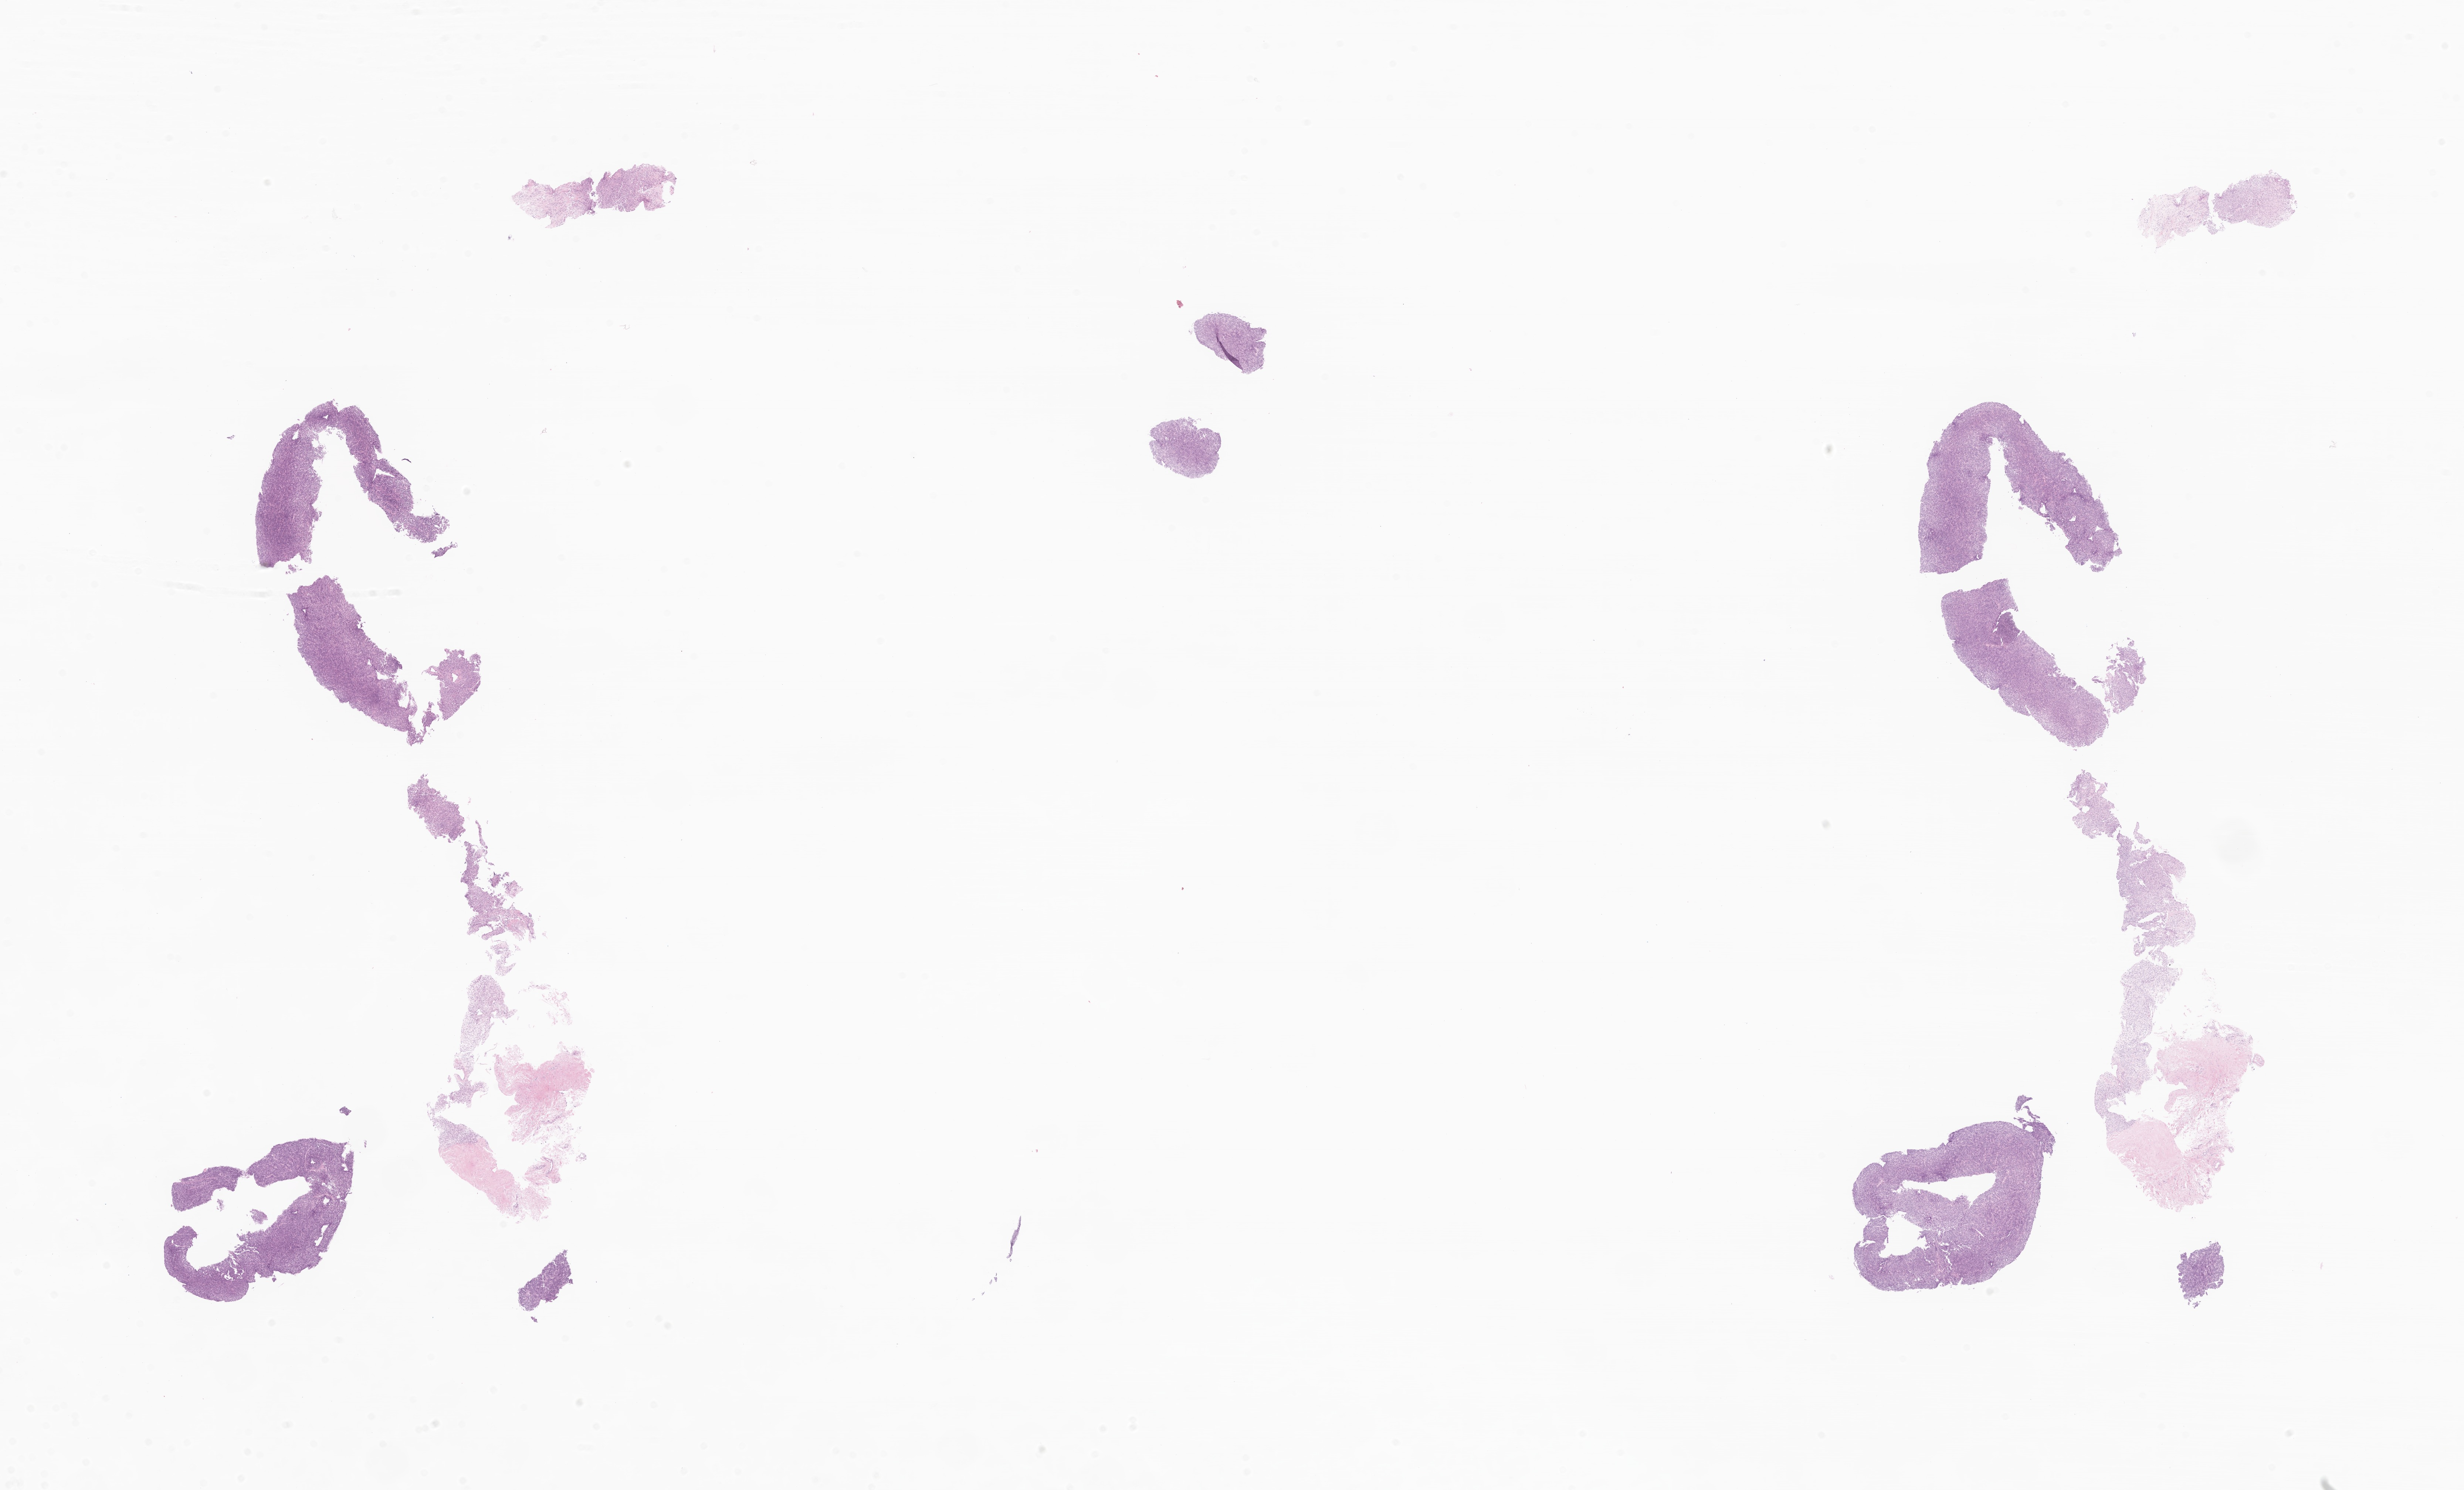
Hematoxylin and eosin (H&E) whole-slide image of tumor tissue from the soft tissue of lower extremity, a low-resolution overview of the entire scanned area, about 28.1 x 17.0 mm, formalin-fixed, paraffin-embedded (FFPE) tissue. Female patient, age 177 months.
* diagnosis (ICD-O-3 morphology term): Spindle cell sarcoma